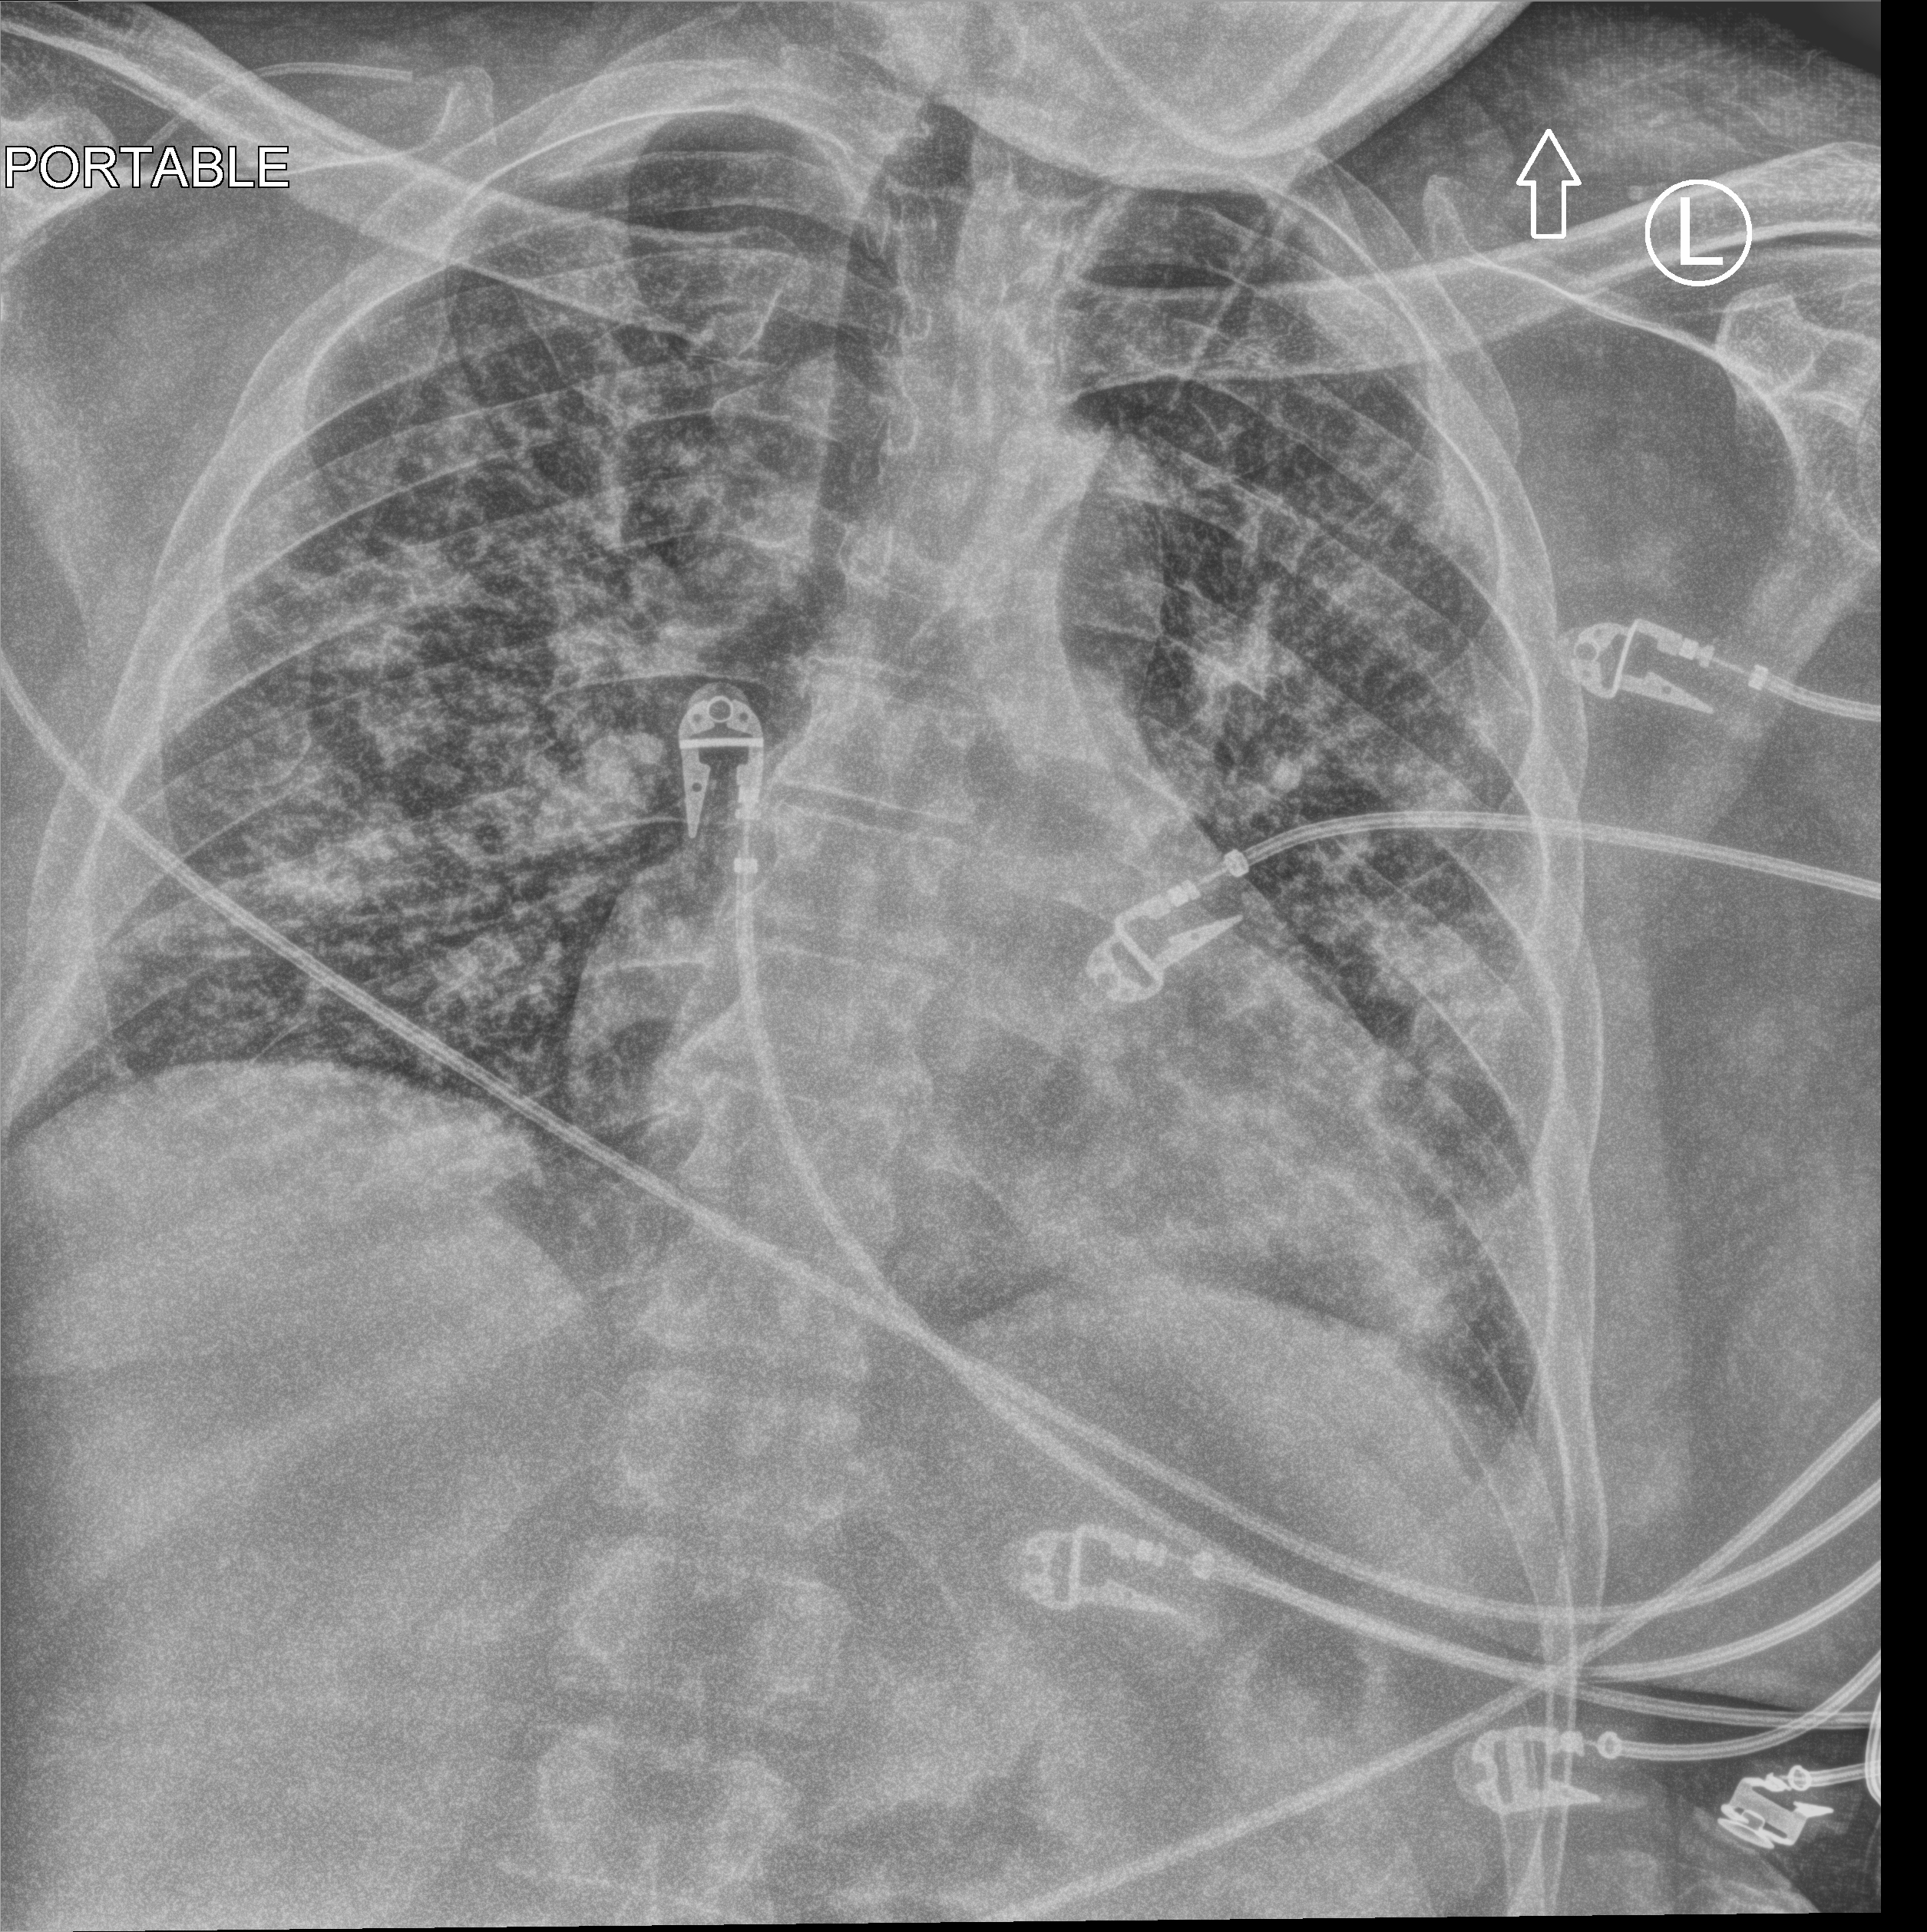
Portable chest radiograph, anteroposterior (AP) projection. Patient hospitalised with COVID-19; male, aged 18–59 years.
Admission-level facts for this patient (not findings on this image; timing relative to this image not recorded): length of hospital stay: 15 days; admitted to intensive care during this hospital stay: yes.